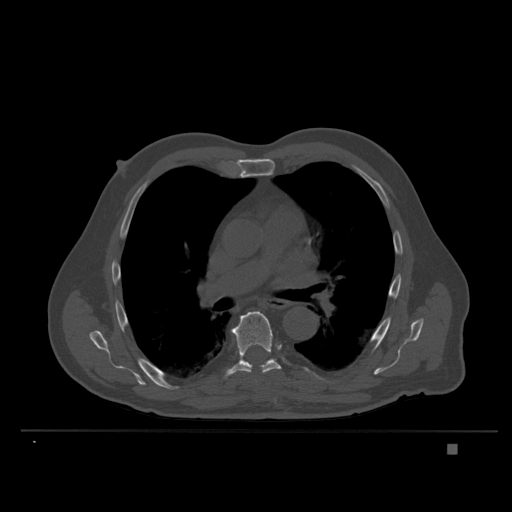
CT including the spine, one axial slice; position 245 of 435 along the scan axis; bone window (W 1800 / L 400 HU); 1.5 mm slice thickness; 512 × 512 image matrix, field of view 434 × 434 mm. Male patient, age 73 years. From the clinical record (not read from this slice): primary cancer: skin.
Outlined on this slice (semi-automatic segmentation, software-assisted and operator-edited):
- T7 vertebra: bounding box (x1, y1, x2, y2) in pixels: (225, 311, 281, 377)